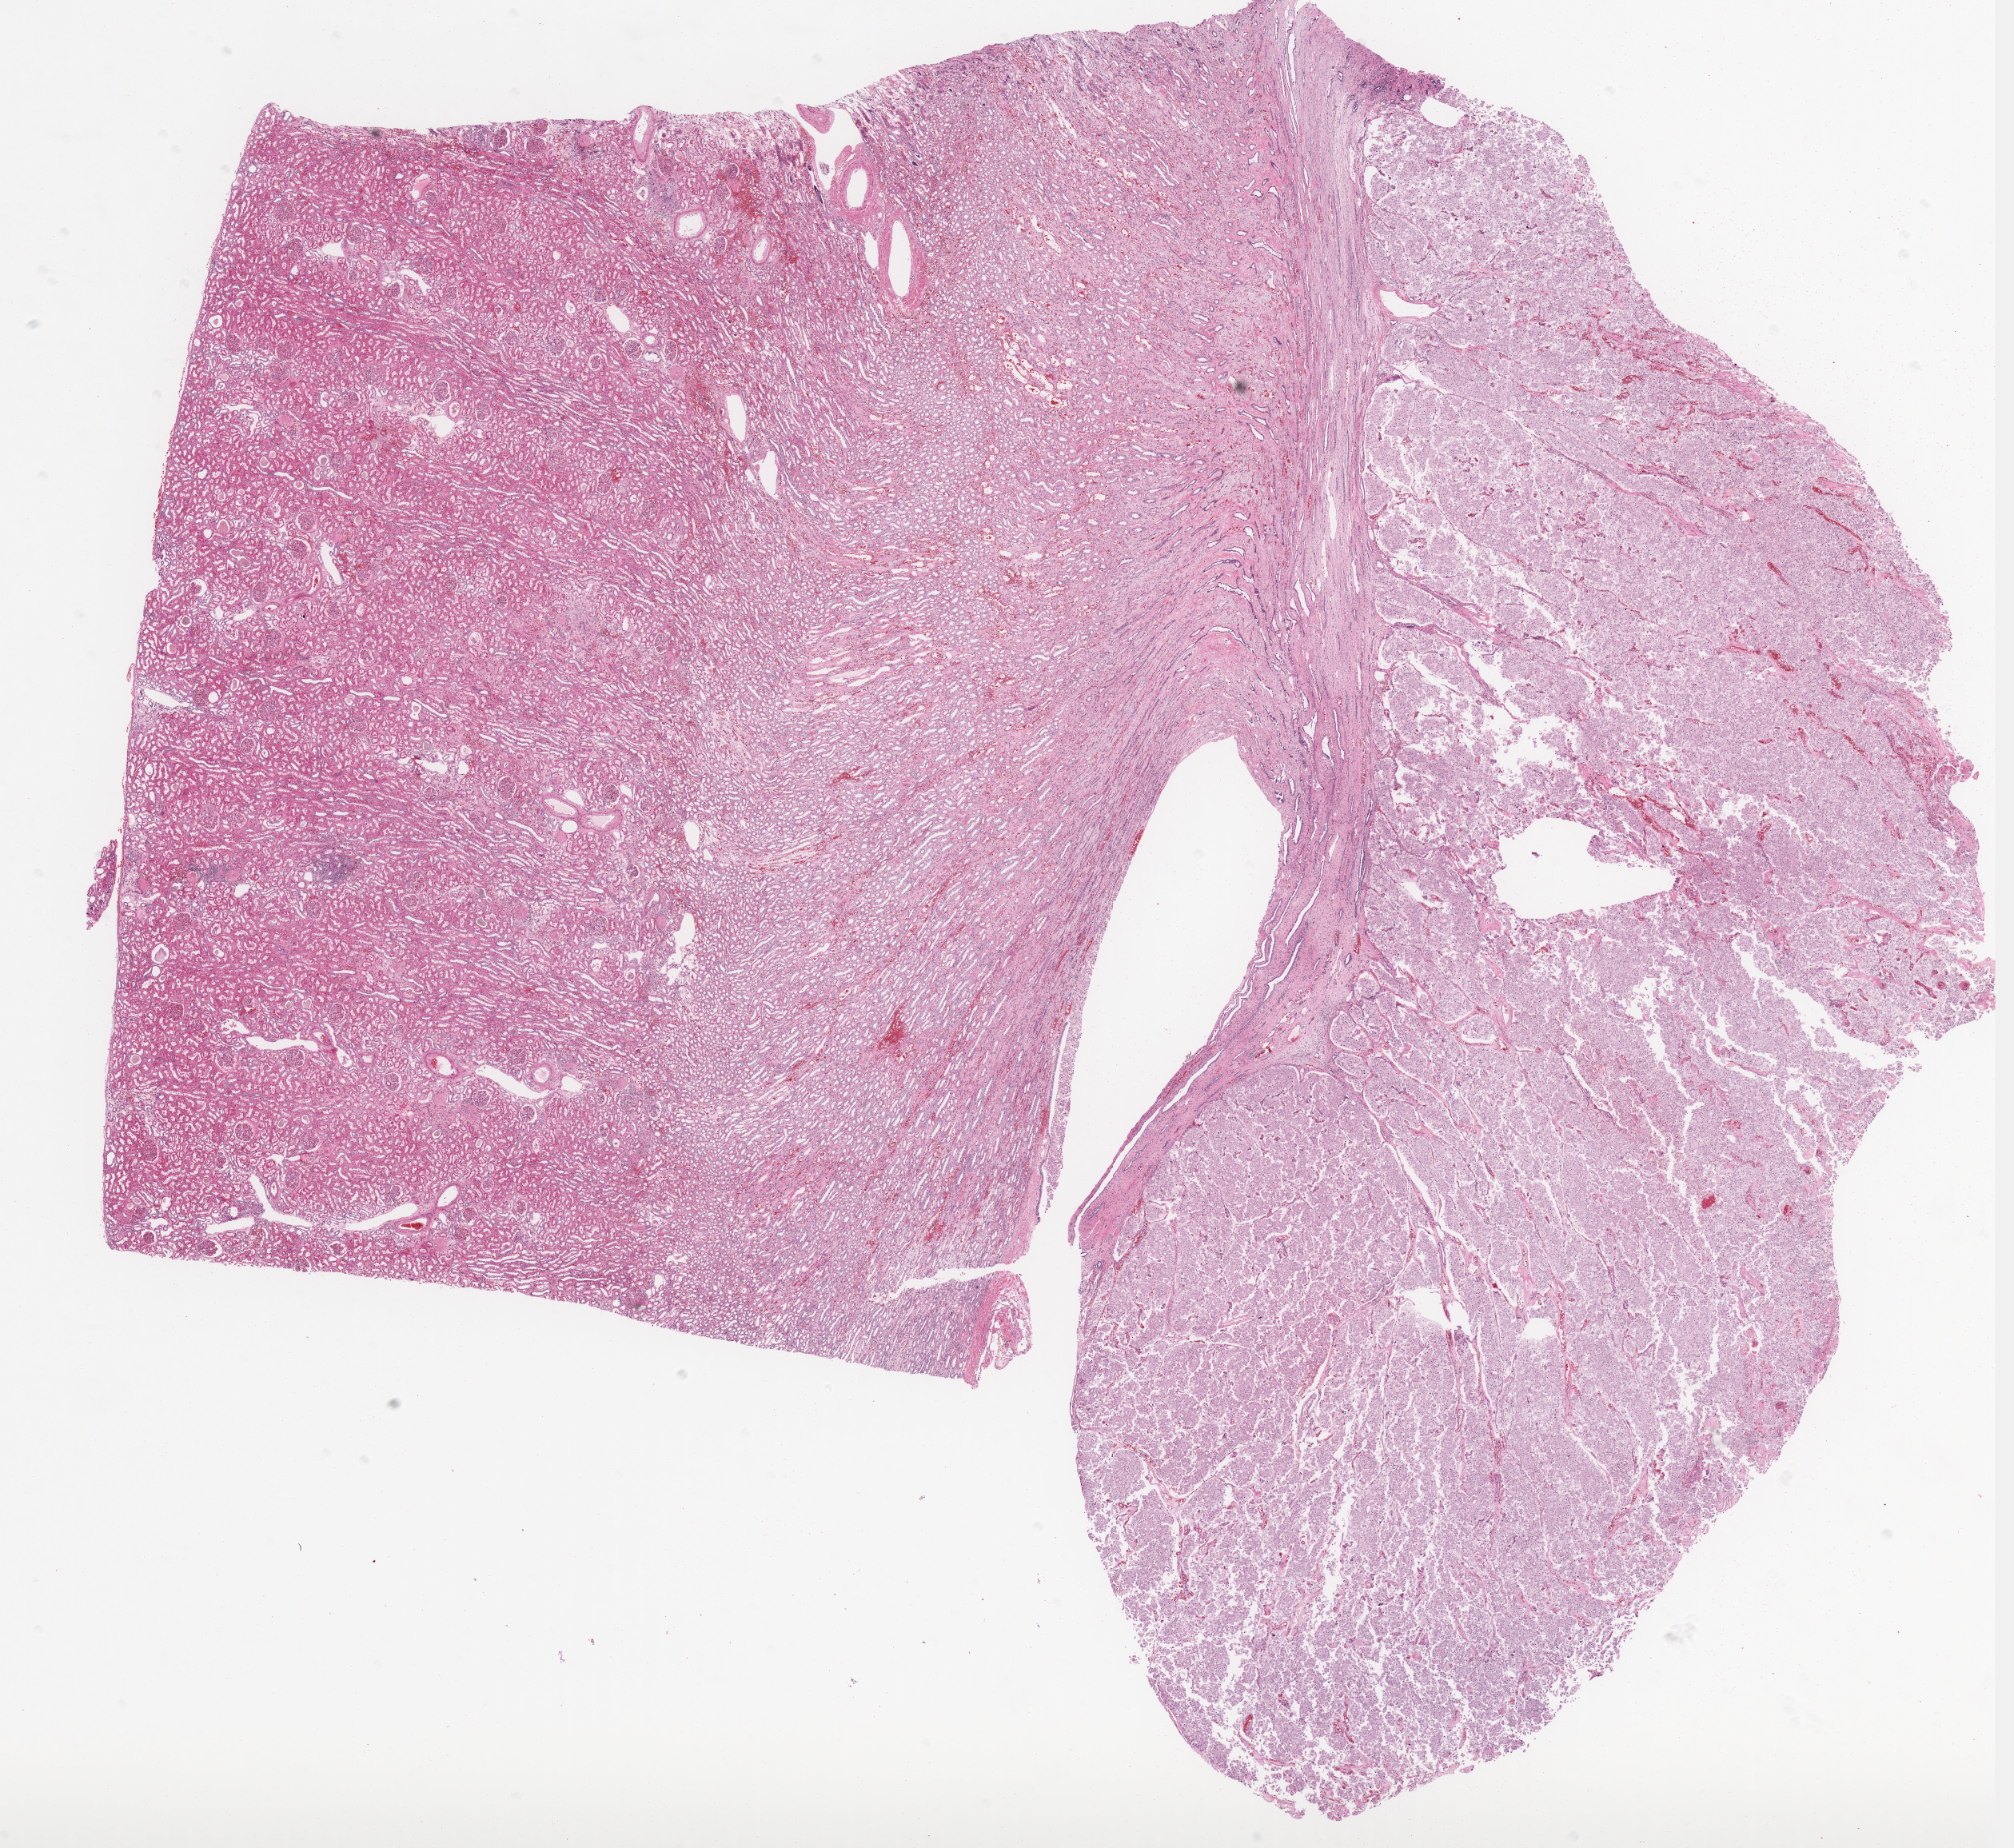
H&E-stained whole-slide image, a low-resolution overview of the entire scanned area, about 20.1 x 18.5 mm, formalin-fixed paraffin-embedded (FFPE) diagnostic section, sample: primary tumour, kidney. Male, age 34 years at initial diagnosis.
* laterality: right
* diagnosis: Renal cell carcinoma, chromophobe type
* AJCC pathologic stage: II (6th edition)
* lymph nodes positive (case pathology): 0 of 13 examined